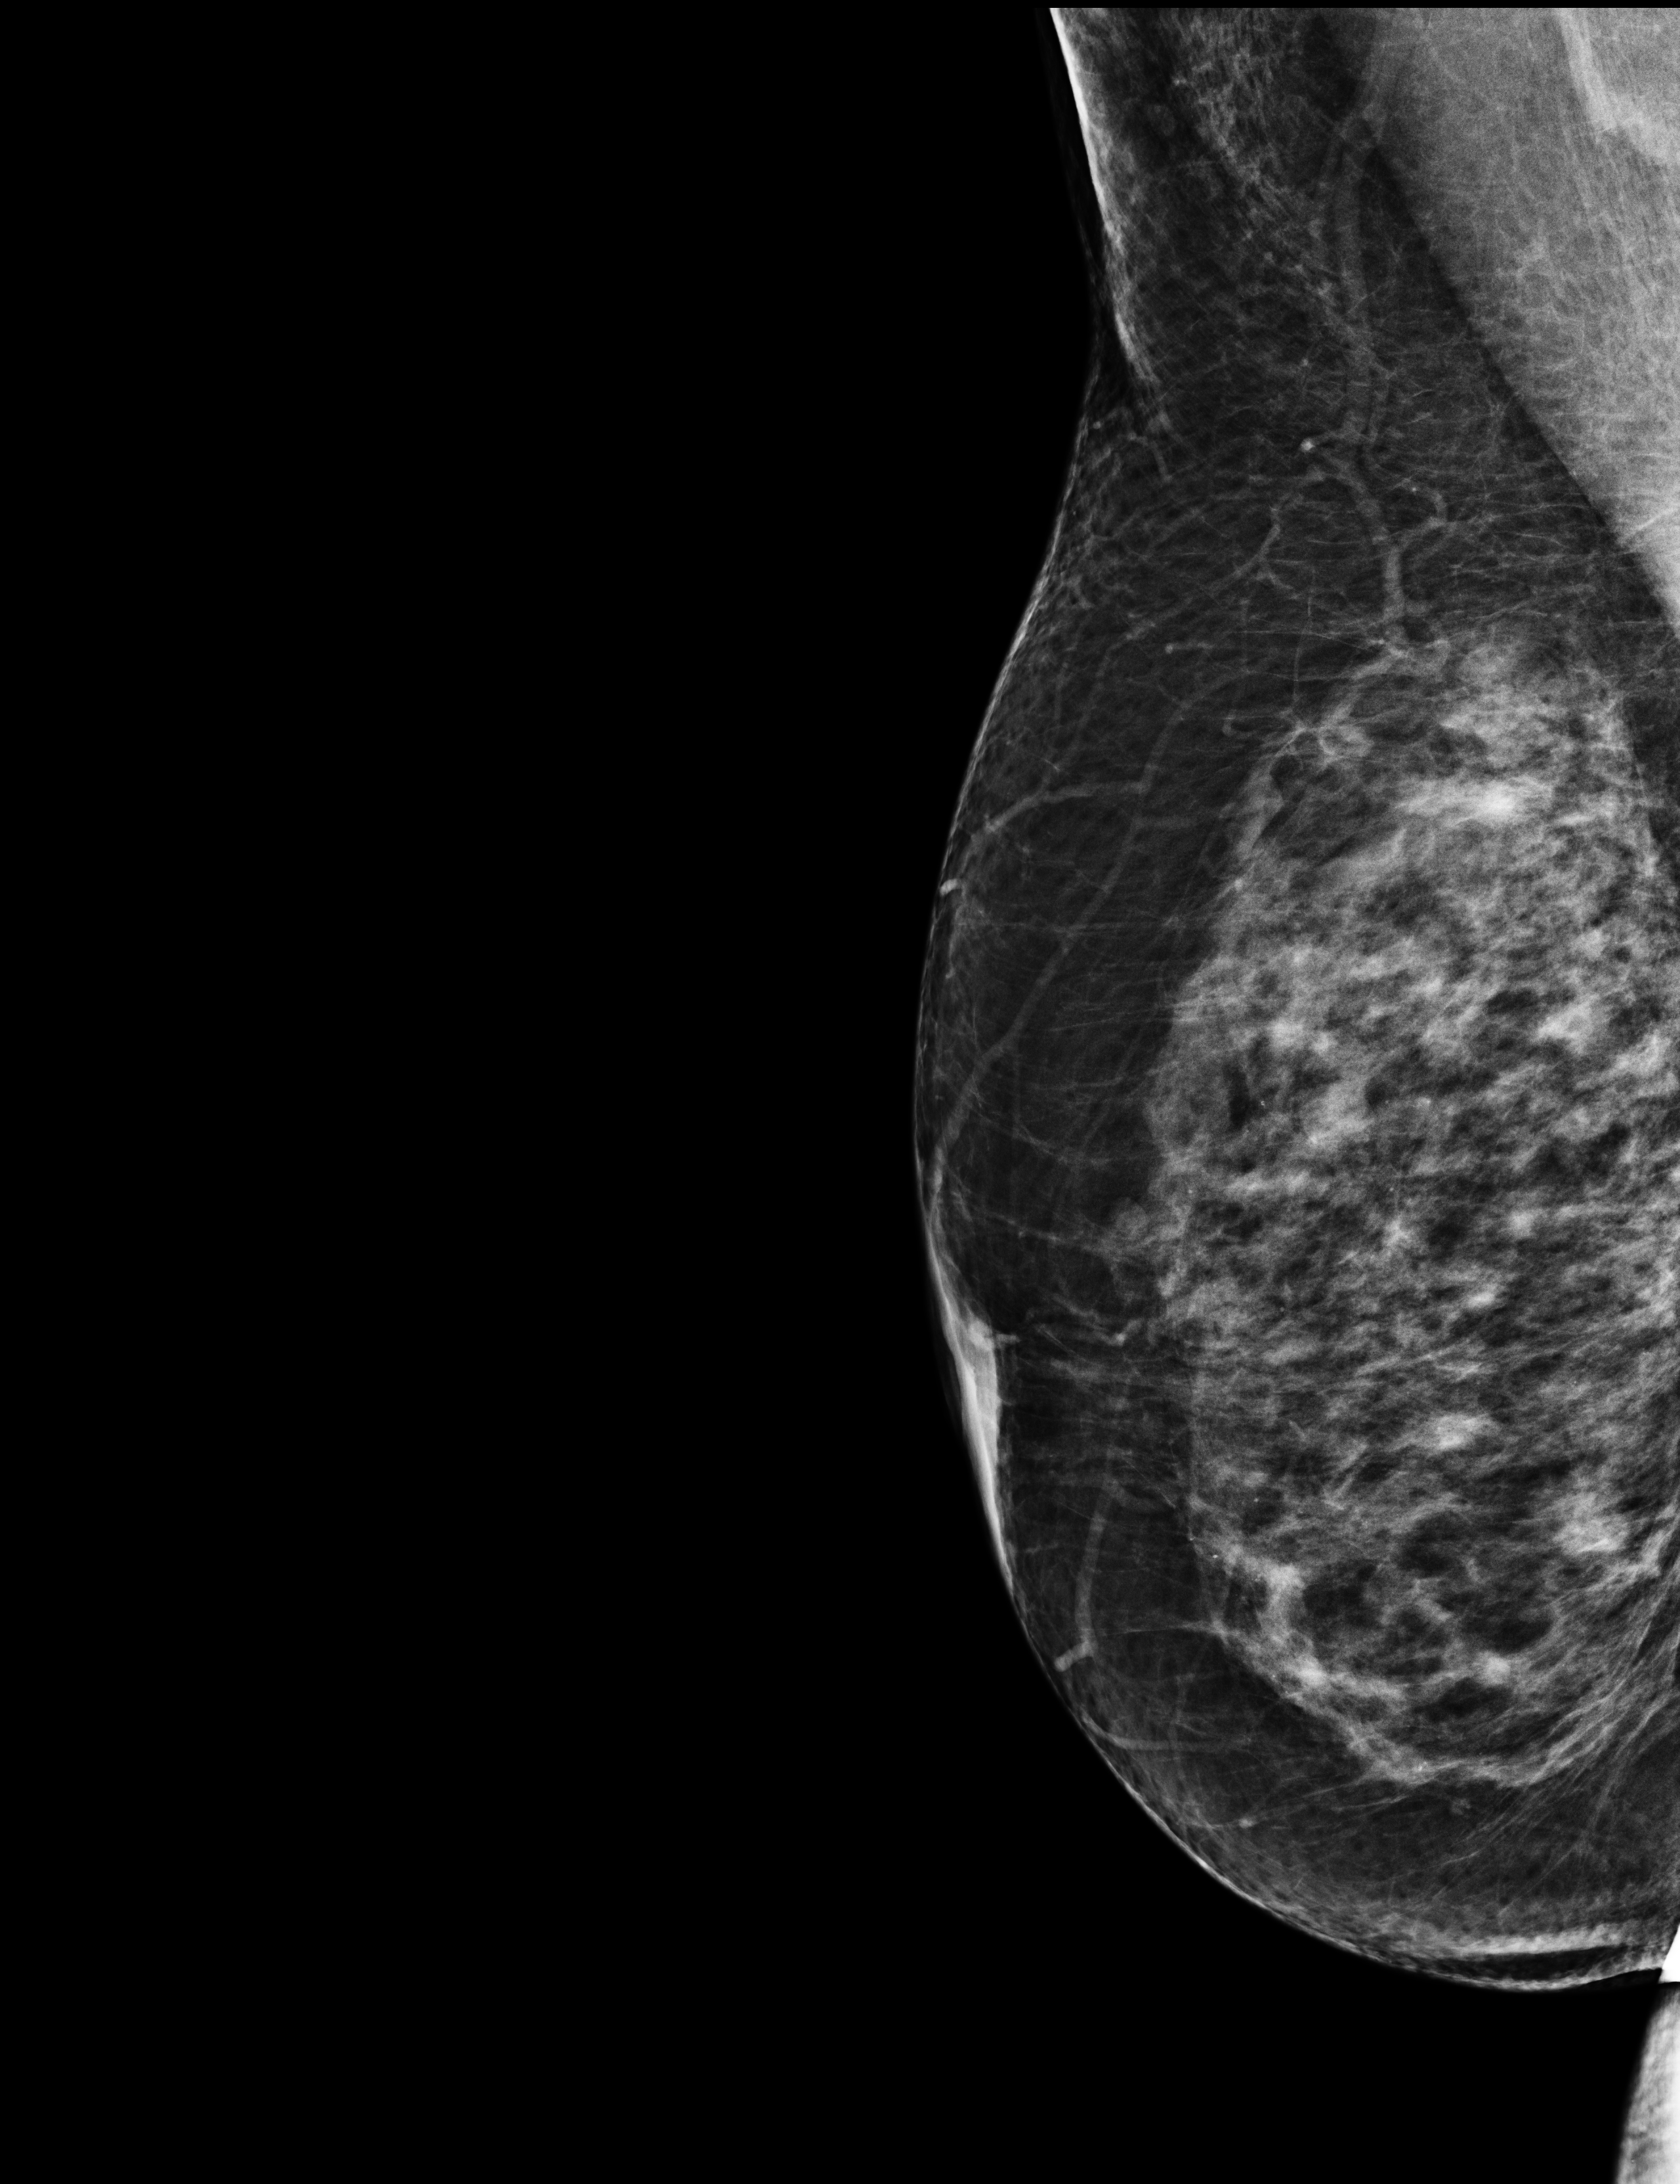
Digital mammogram (FFDM); right breast; MLO view; screening examination; compressed breast thickness 68 mm. Patient aged 70 years (female).
Breast density at the screening exam (both breasts): heterogeneously dense (BI-RADS density category c). Final BI-RADS assessment for this screening round (tomosynthesis exam, both breasts): category 2. Recall: no recall after this screen.